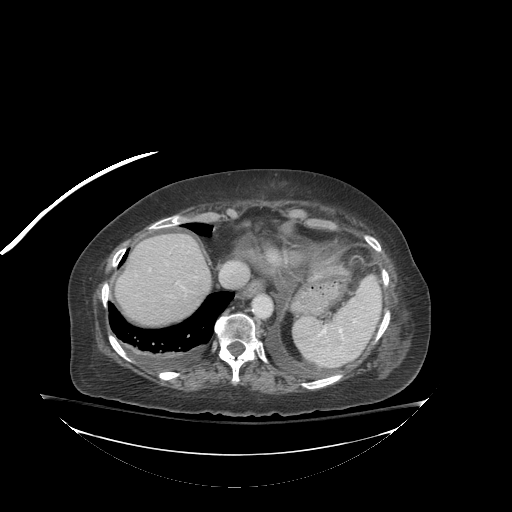
Contrast-enhanced abdominal CT (liver protocol), one axial slice. Slice 71 of 81 in the series (ordered by position). Reconstruction kernel STANDARD. 140 kVp. Soft-tissue window (W 400 / L 40 HU). 2.5 mm slice thickness. 512 × 512 image matrix, field of view 500 × 500 mm. Case-level facts recorded for this patient, not image findings: diagnosis: hepatocellular carcinoma (patient treated with transarterial chemoembolisation; whether this scan precedes or follows treatment is not stated here); TNM stage (as recorded): Stage-I.
Structures marked on this image (semi-automatic segmentation, software-assisted and operator-edited):
- abdominal aorta: bounding box <254,296,272,318> (left, top, right, bottom; pixels)
- liver parenchyma outside the tumour (the mass and vessels are separate outlines, so this box may not span the whole liver): <126,234,210,322>
- liver vessels: <149,268,184,289>